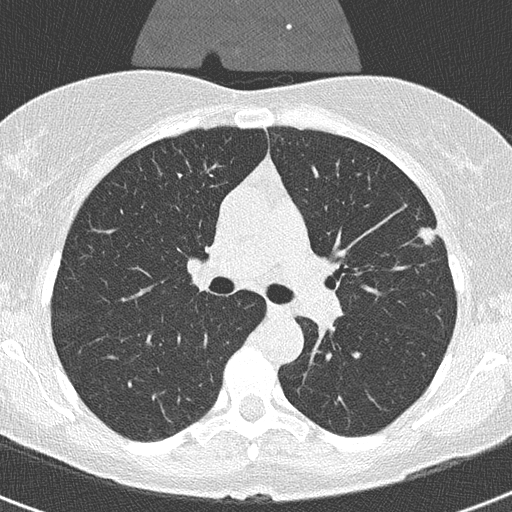
Low-dose screening chest CT, one axial slice. Position 210 of 320 along the scan axis. Reconstruction kernel B50f. Lung window (W 1500 / L -600 HU). 2 mm slice thickness. 512 × 512 image matrix, field of view 290 × 290 mm.
Structures marked on this image (manually delineated by an expert):
- lesion 1 (tumor, upper lobe of left lung): bounding box <419,227,435,244> (left, top, right, bottom; pixels)